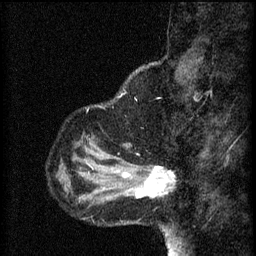
Breast MRI (dynamic contrast-enhanced), one sagittal slice. Position 13 of 60 along the scan axis. 3 images stored at this slice position (order not interpretable as contrast timing). 1.5 T. TE 4.2 ms, TR 8.2 ms. 2 mm slice thickness. 256 × 256 image matrix, field of view 180 × 180 mm. Patient: female, 37 years.
Outlined on this slice (semi-automatic segmentation, software-assisted and operator-edited):
- analysis volume of interest (the breast-tissue region the enhancement analysis was run in; not a lesion): bounding box <126,164,175,201> (left, top, right, bottom; pixels)
- tumour enhancement mask (voxels above the 70 % enhancement threshold inside the analysis volume of interest): <126,168,175,199>